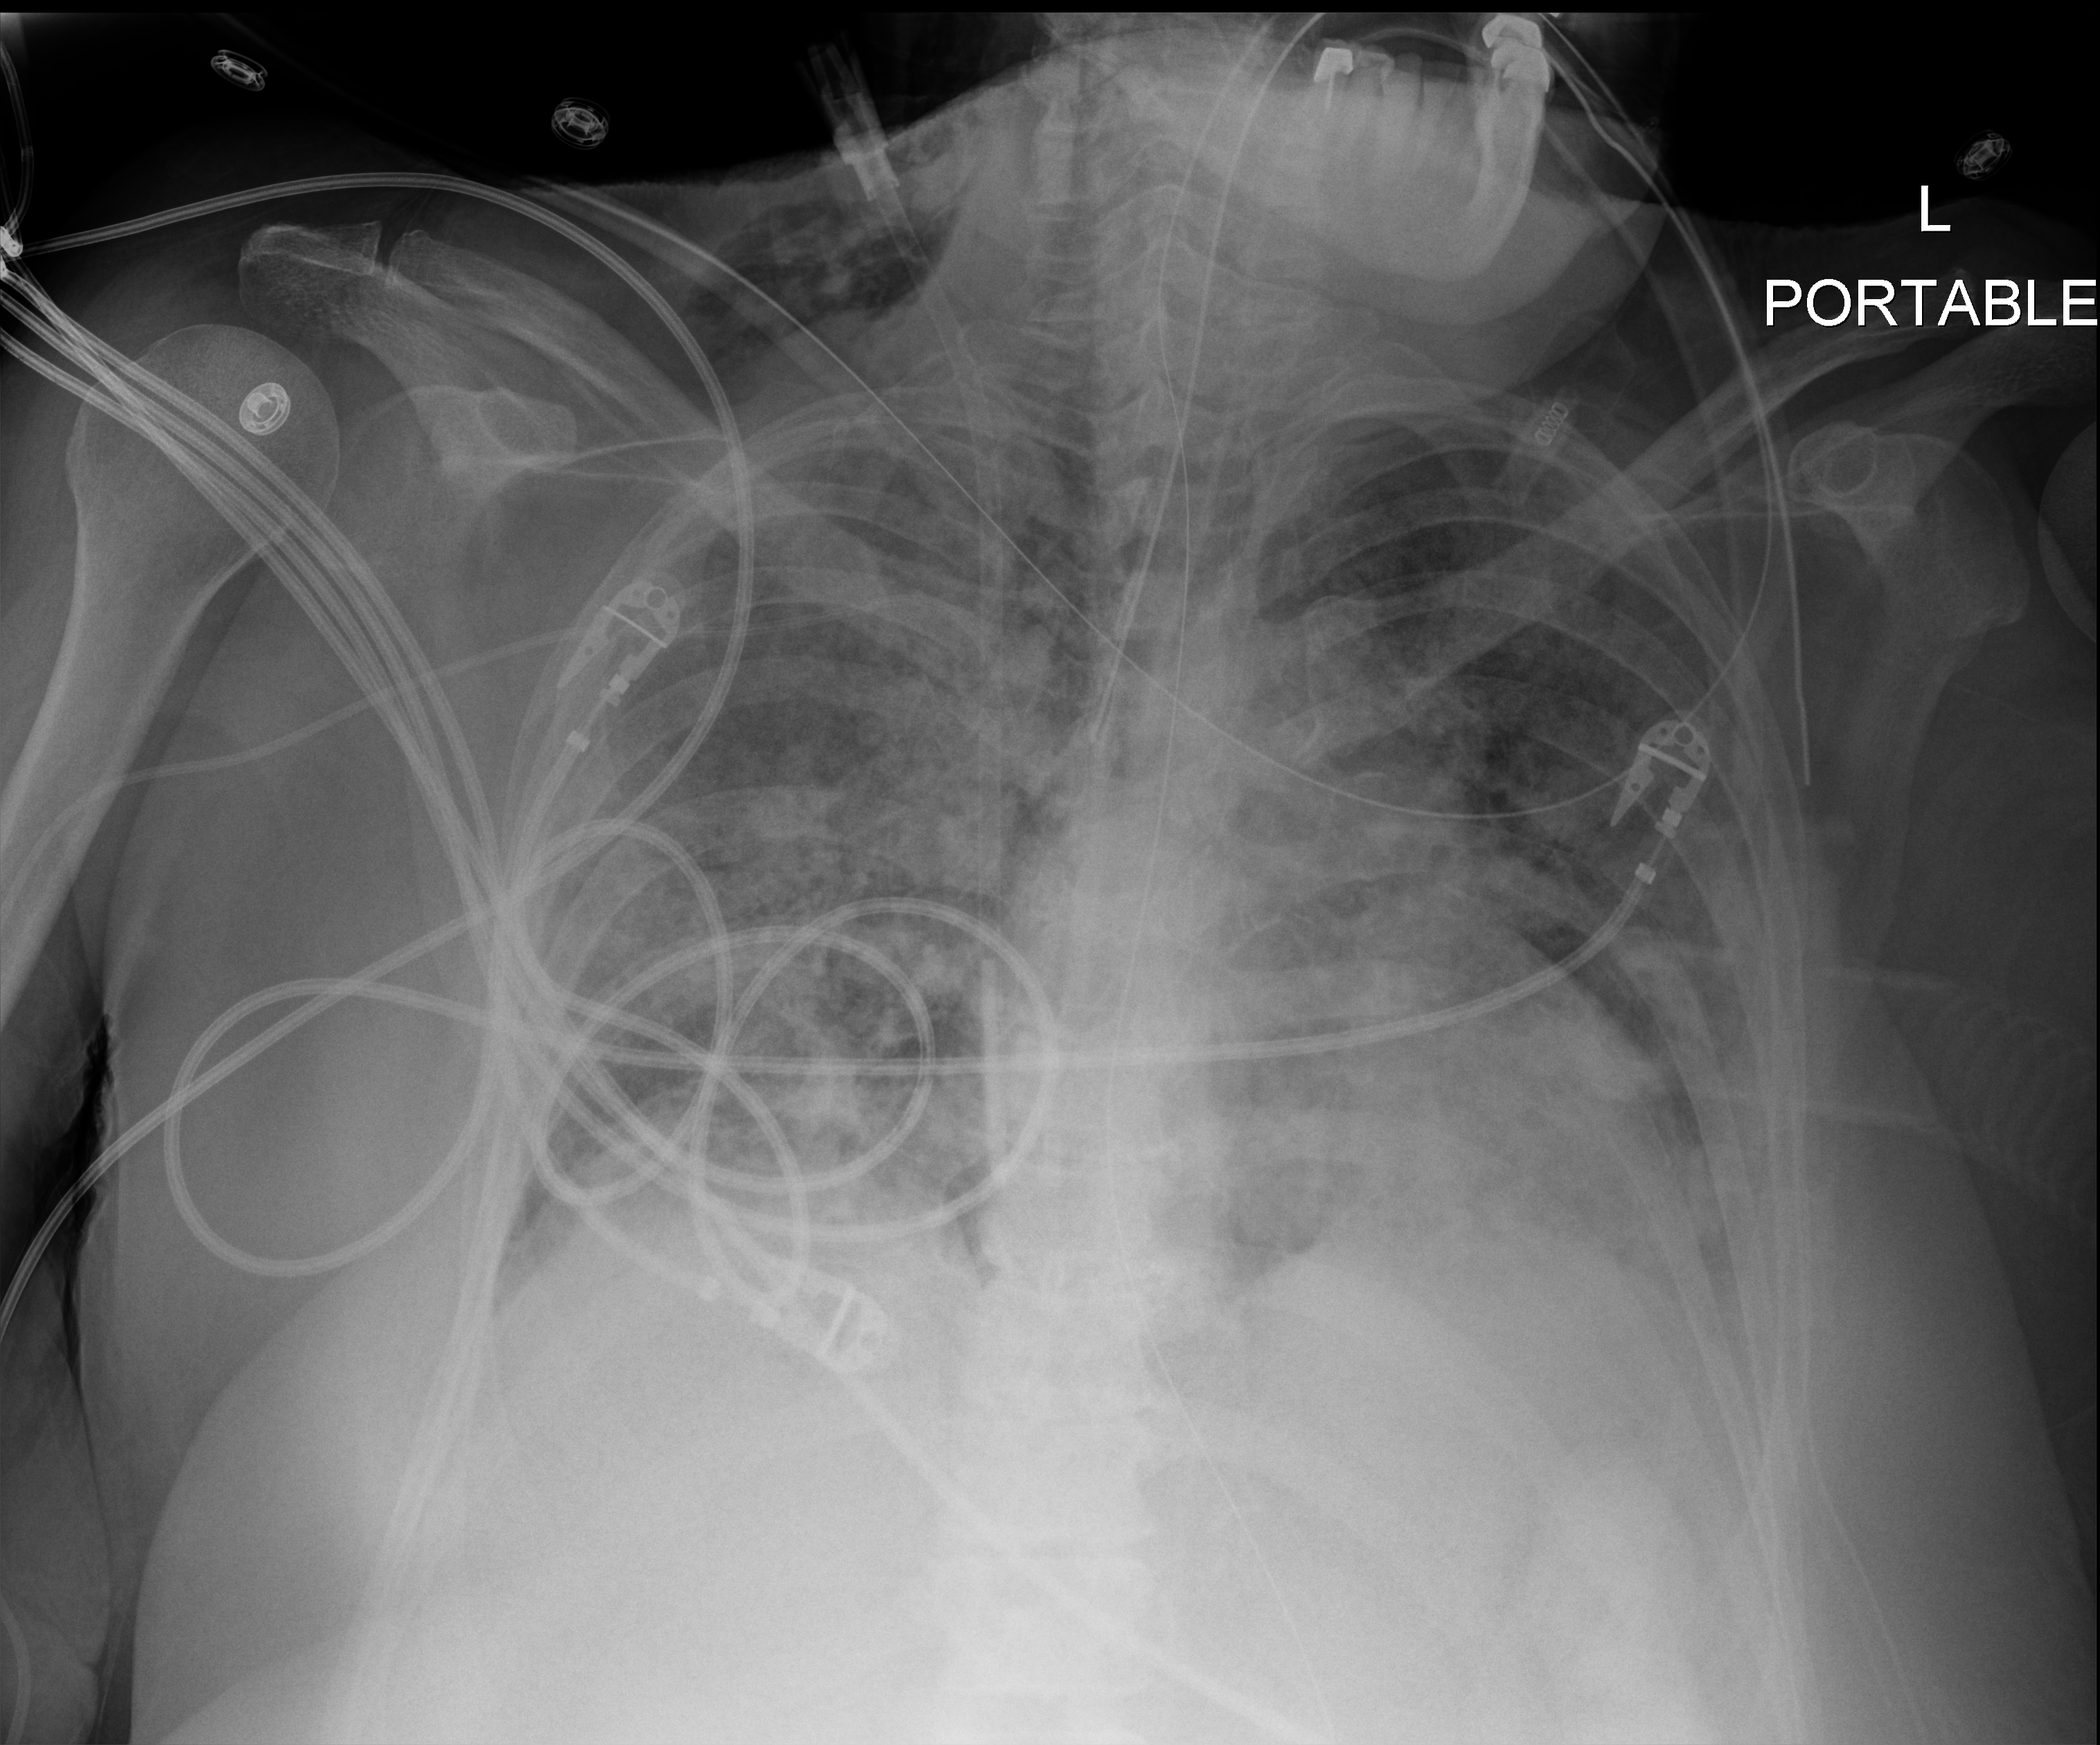
Chest radiograph (digital radiography). Patient hospitalised with COVID-19; female, aged 60–74 years.
Admission-level facts for this patient (not findings on this image; timing relative to this image not recorded): admitted to intensive care during this hospital stay: yes; diabetes (admission record): no; mechanically ventilated during this hospital stay: yes.